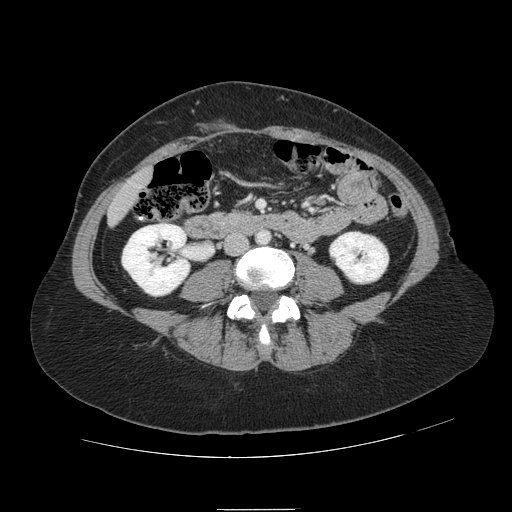
Contrast-enhanced abdominal CT, one axial slice; position 4 of 121 along the scan axis; intravenous contrast given; soft-tissue window (W 400 / L 40 HU); 2.5 mm slice thickness; 512 × 512 image matrix. Female patient, age 52 years. From the clinical record (not read from this slice): diagnosis: colorectal cancer liver metastases, imaged before liver resection; multiple liver metastases: yes.
Outlined on this slice (manually delineated by an expert):
- liver: bounding box [x1, y1, x2, y2] px = [111, 171, 150, 222]